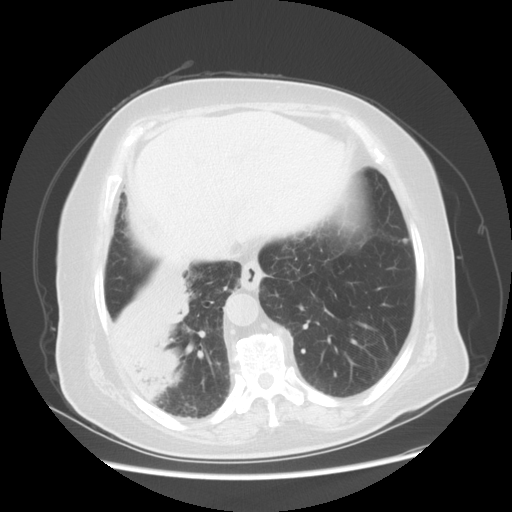
Chest CT, one axial slice; position 15 of 56 along the scan axis; lung window (W 1500 / L -600 HU); 512 × 512 image matrix, field of view 378 × 378 mm. Female patient, age 73 years. Case-level facts recorded for this patient, not image findings: clinical TNM (as recorded): T3 N0 M0.
Annotated regions visible in this slice (rectangle marked by the reading radiologist):
- lung tumour (recorded histology: adenocarcinoma): bounding box <101,266,194,400> (left, top, right, bottom; pixels)